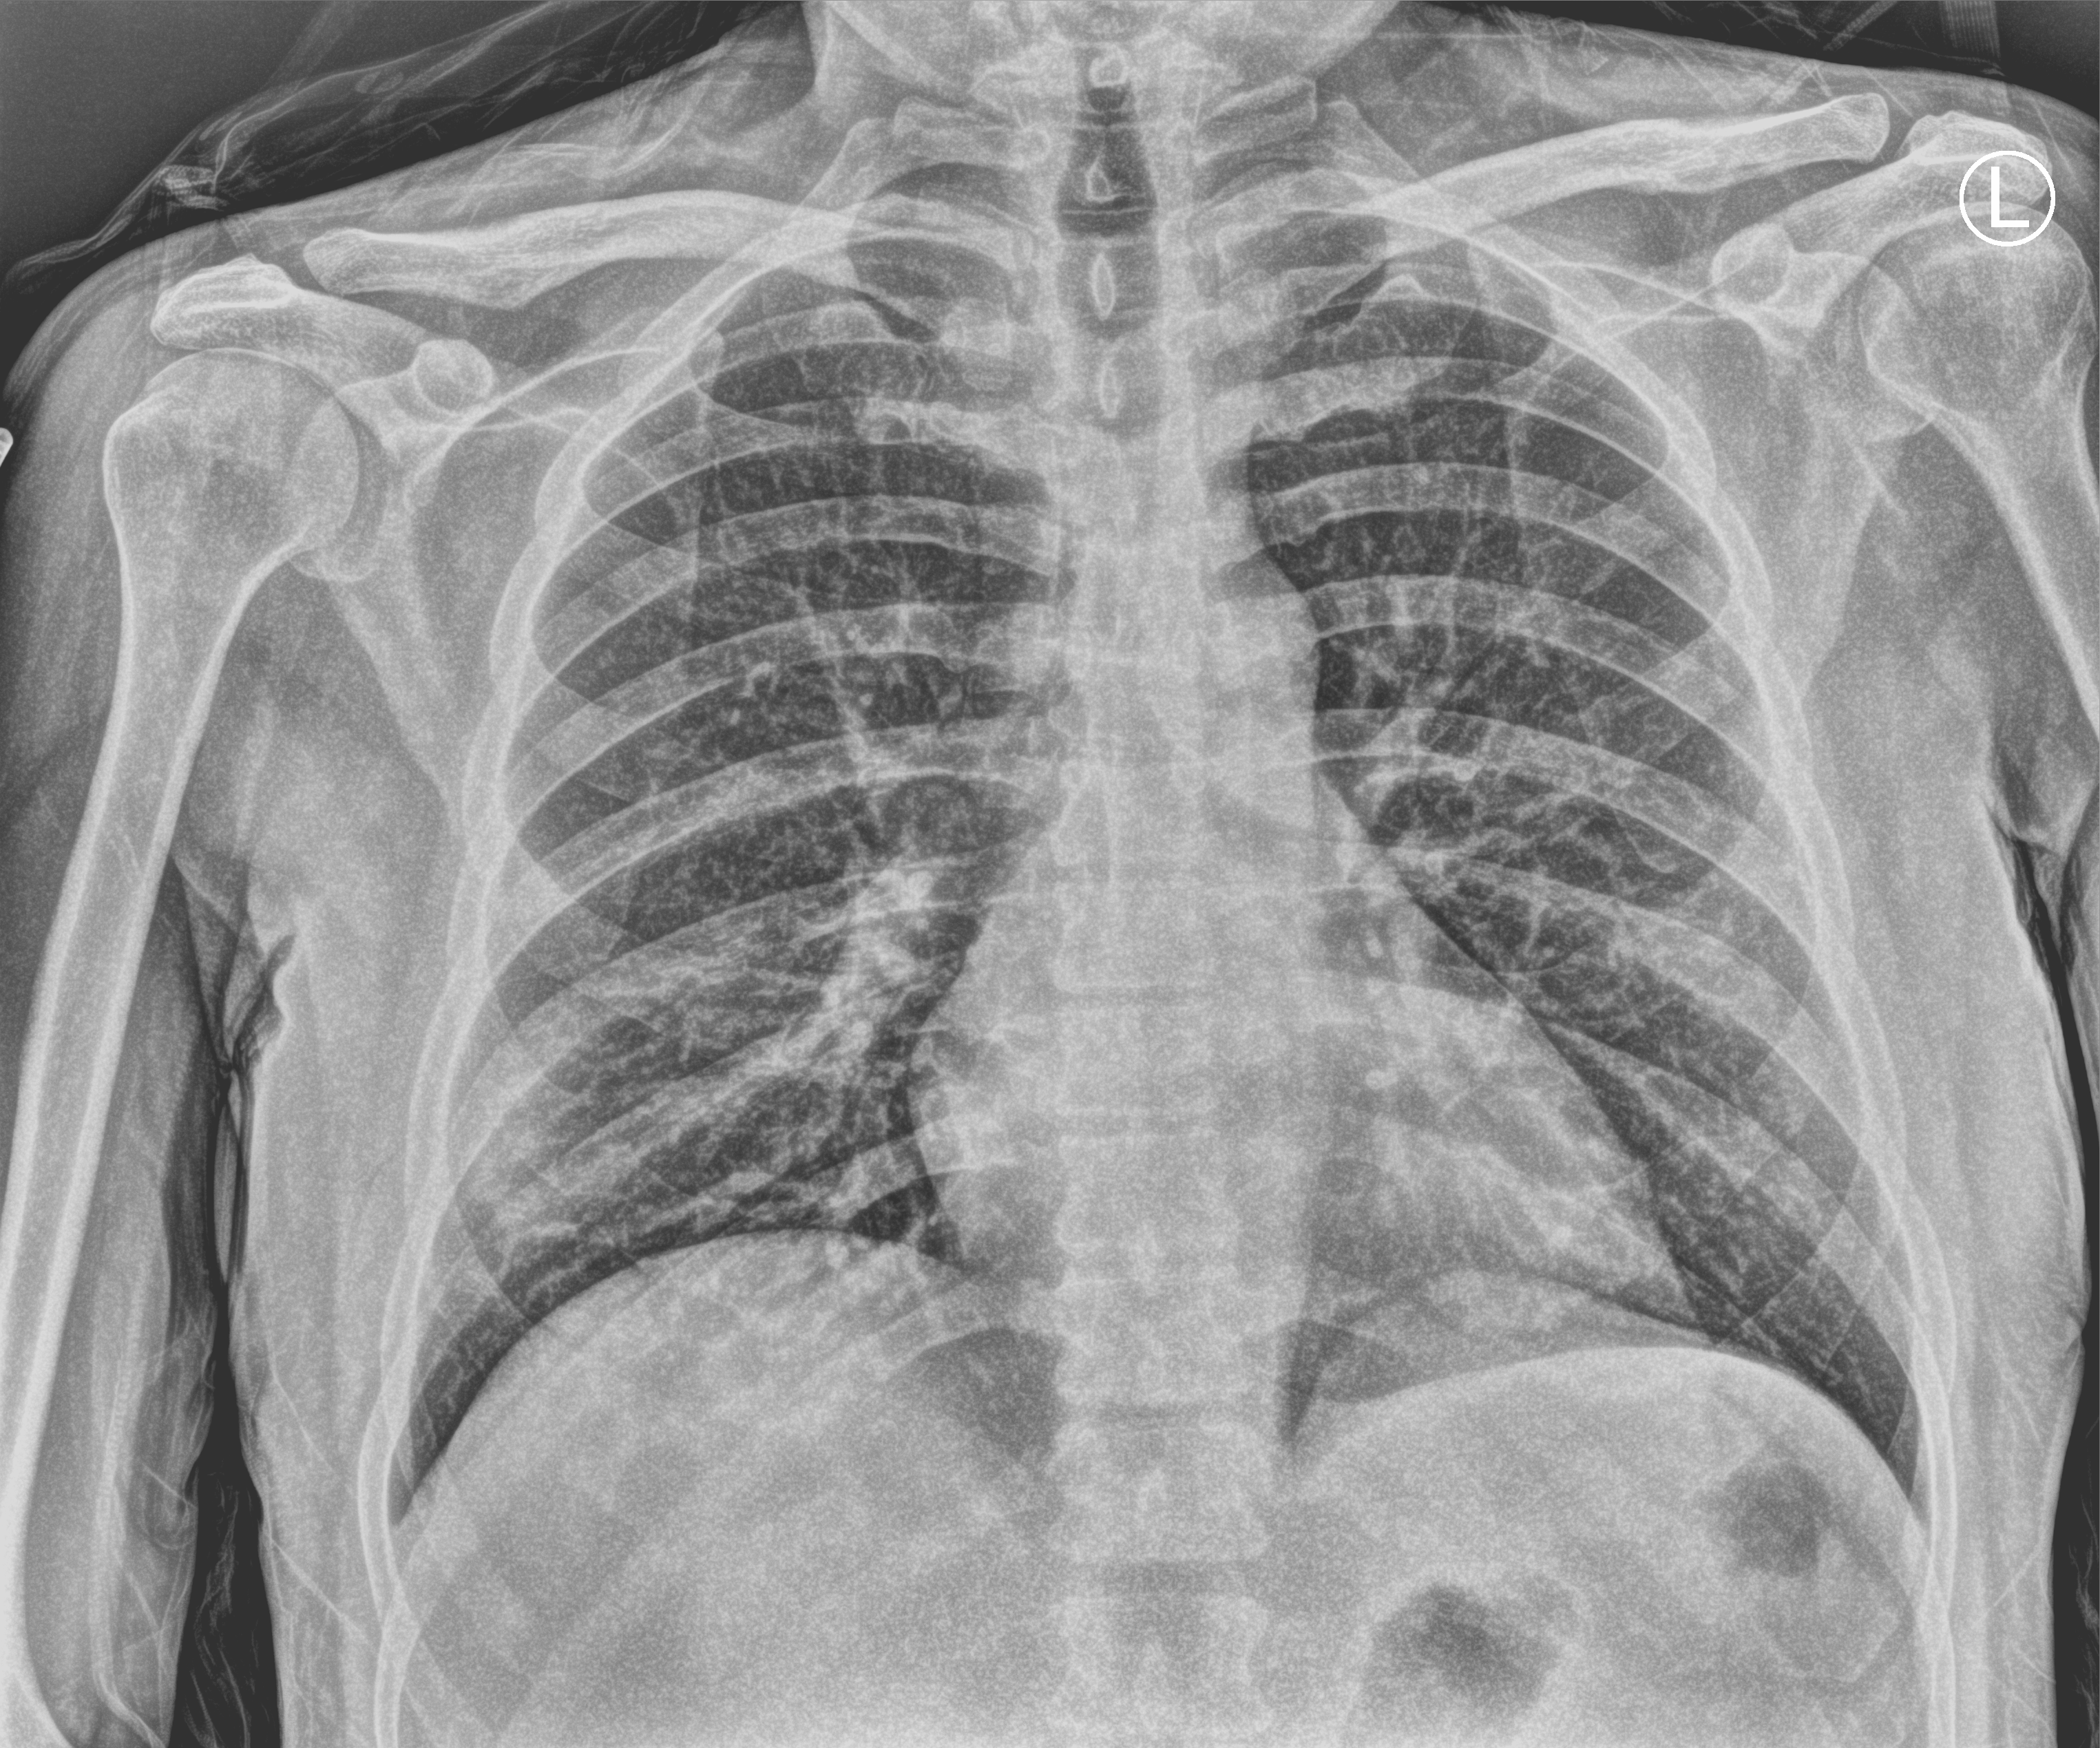
Bedside chest radiograph (computed radiography); anteroposterior (AP) projection. Patient hospitalised with COVID-19; male, aged 18–59 years.
Admission-level facts for this patient (not findings on this image; timing relative to this image not recorded):
- mechanically ventilated during this hospital stay: no